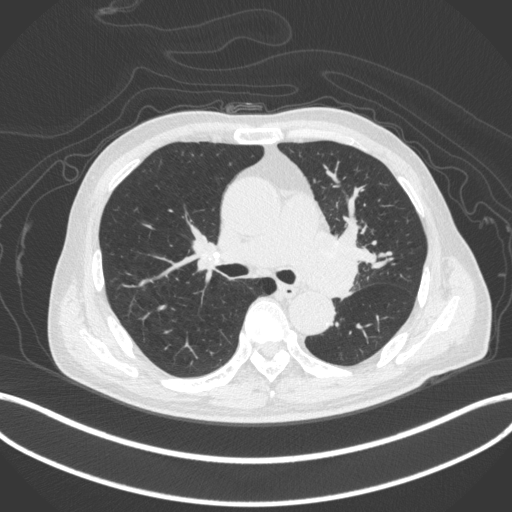
Chest CT, one axial slice; slice 266 of 420 in the series (ordered by position); 120 kVp; lung window (W 1500 / L -600 HU); 1 mm slice thickness; 512 × 512 image matrix, field of view 400 × 400 mm. Male patient, age 77 years. Case-level facts recorded for this patient, not image findings: clinical TNM (as recorded): T3 N1 M0.
Structures marked on this image (rectangle marked by the reading radiologist):
- lung tumour (recorded histology: adenocarcinoma): bounding box [x1, y1, x2, y2] px = [293, 220, 361, 302]